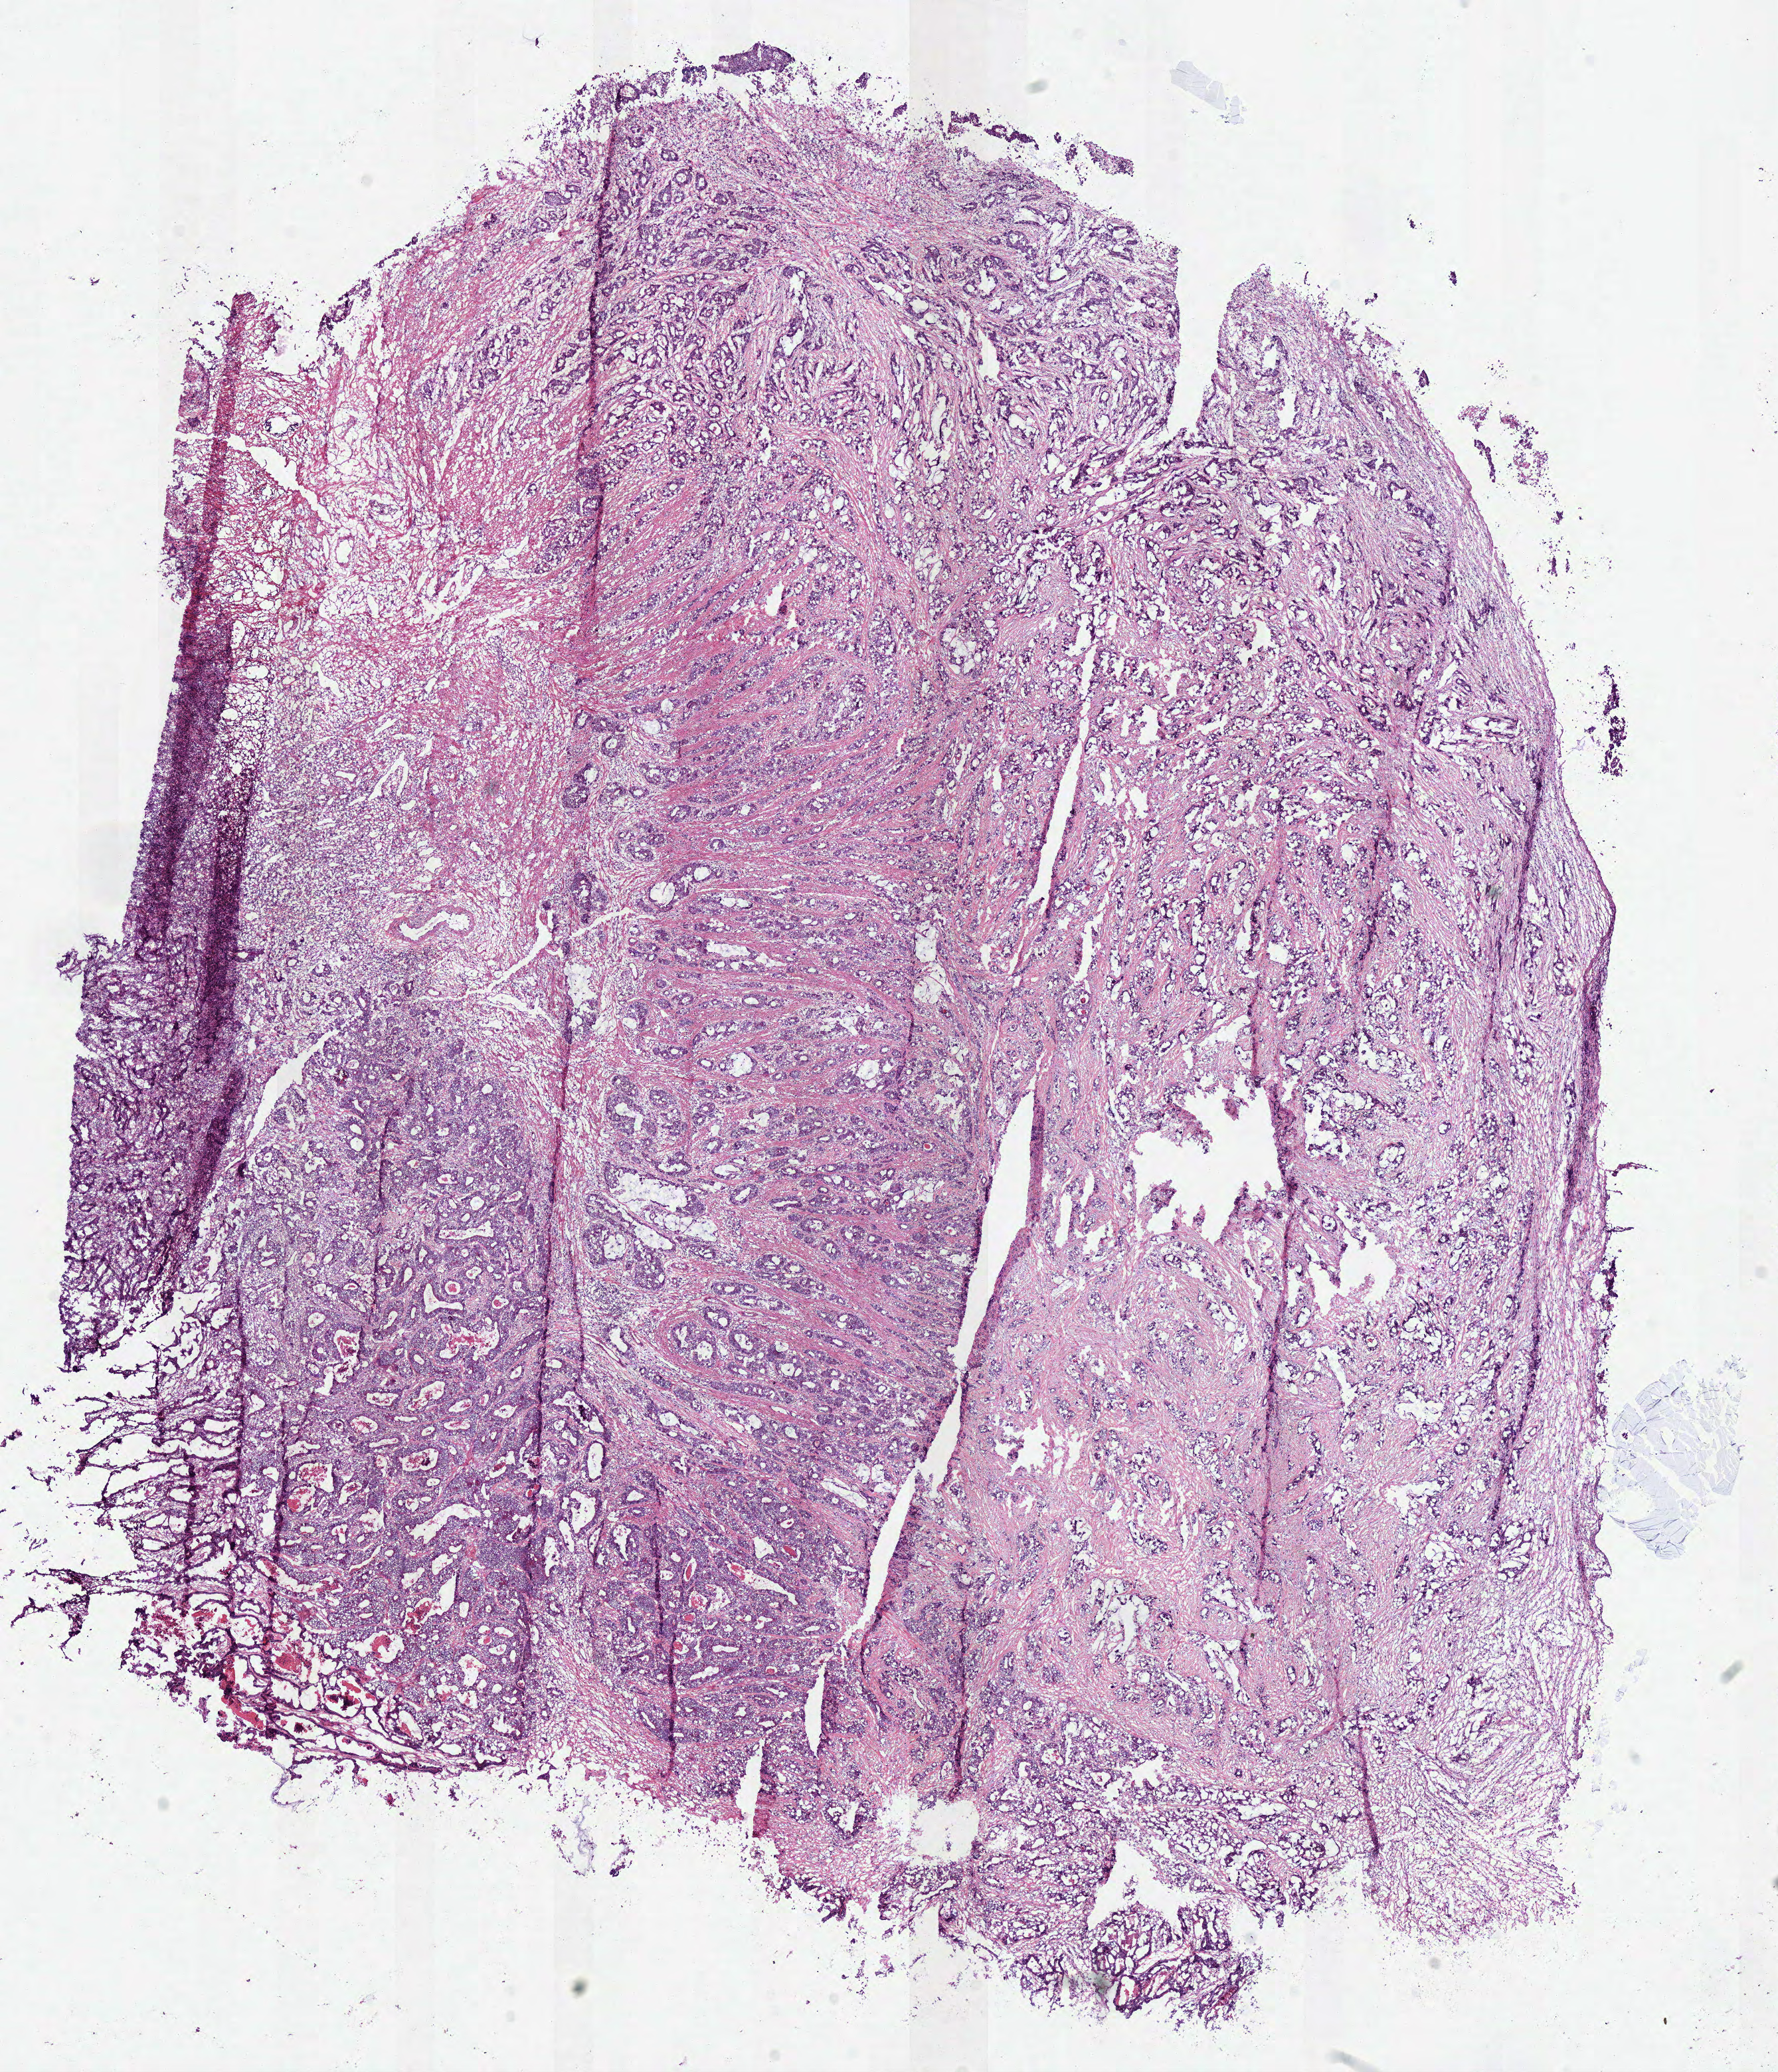
Whole-slide histology image, H&E — shown as a low-resolution overview of the whole scanned area (about 10.5 x 12.3 mm). Frozen section from the top of the tissue portion. Sample: primary tumour, rectum. Female, age 74 years at initial diagnosis. Composition of this section per pathologist review: tumour cells 75%, tumour nuclei 80%, normal cells 0%, stromal cells 20%, necrosis 5%.
• diagnosis: Adenocarcinoma, NOS
• AJCC pathologic stage: IIIB (7th edition)